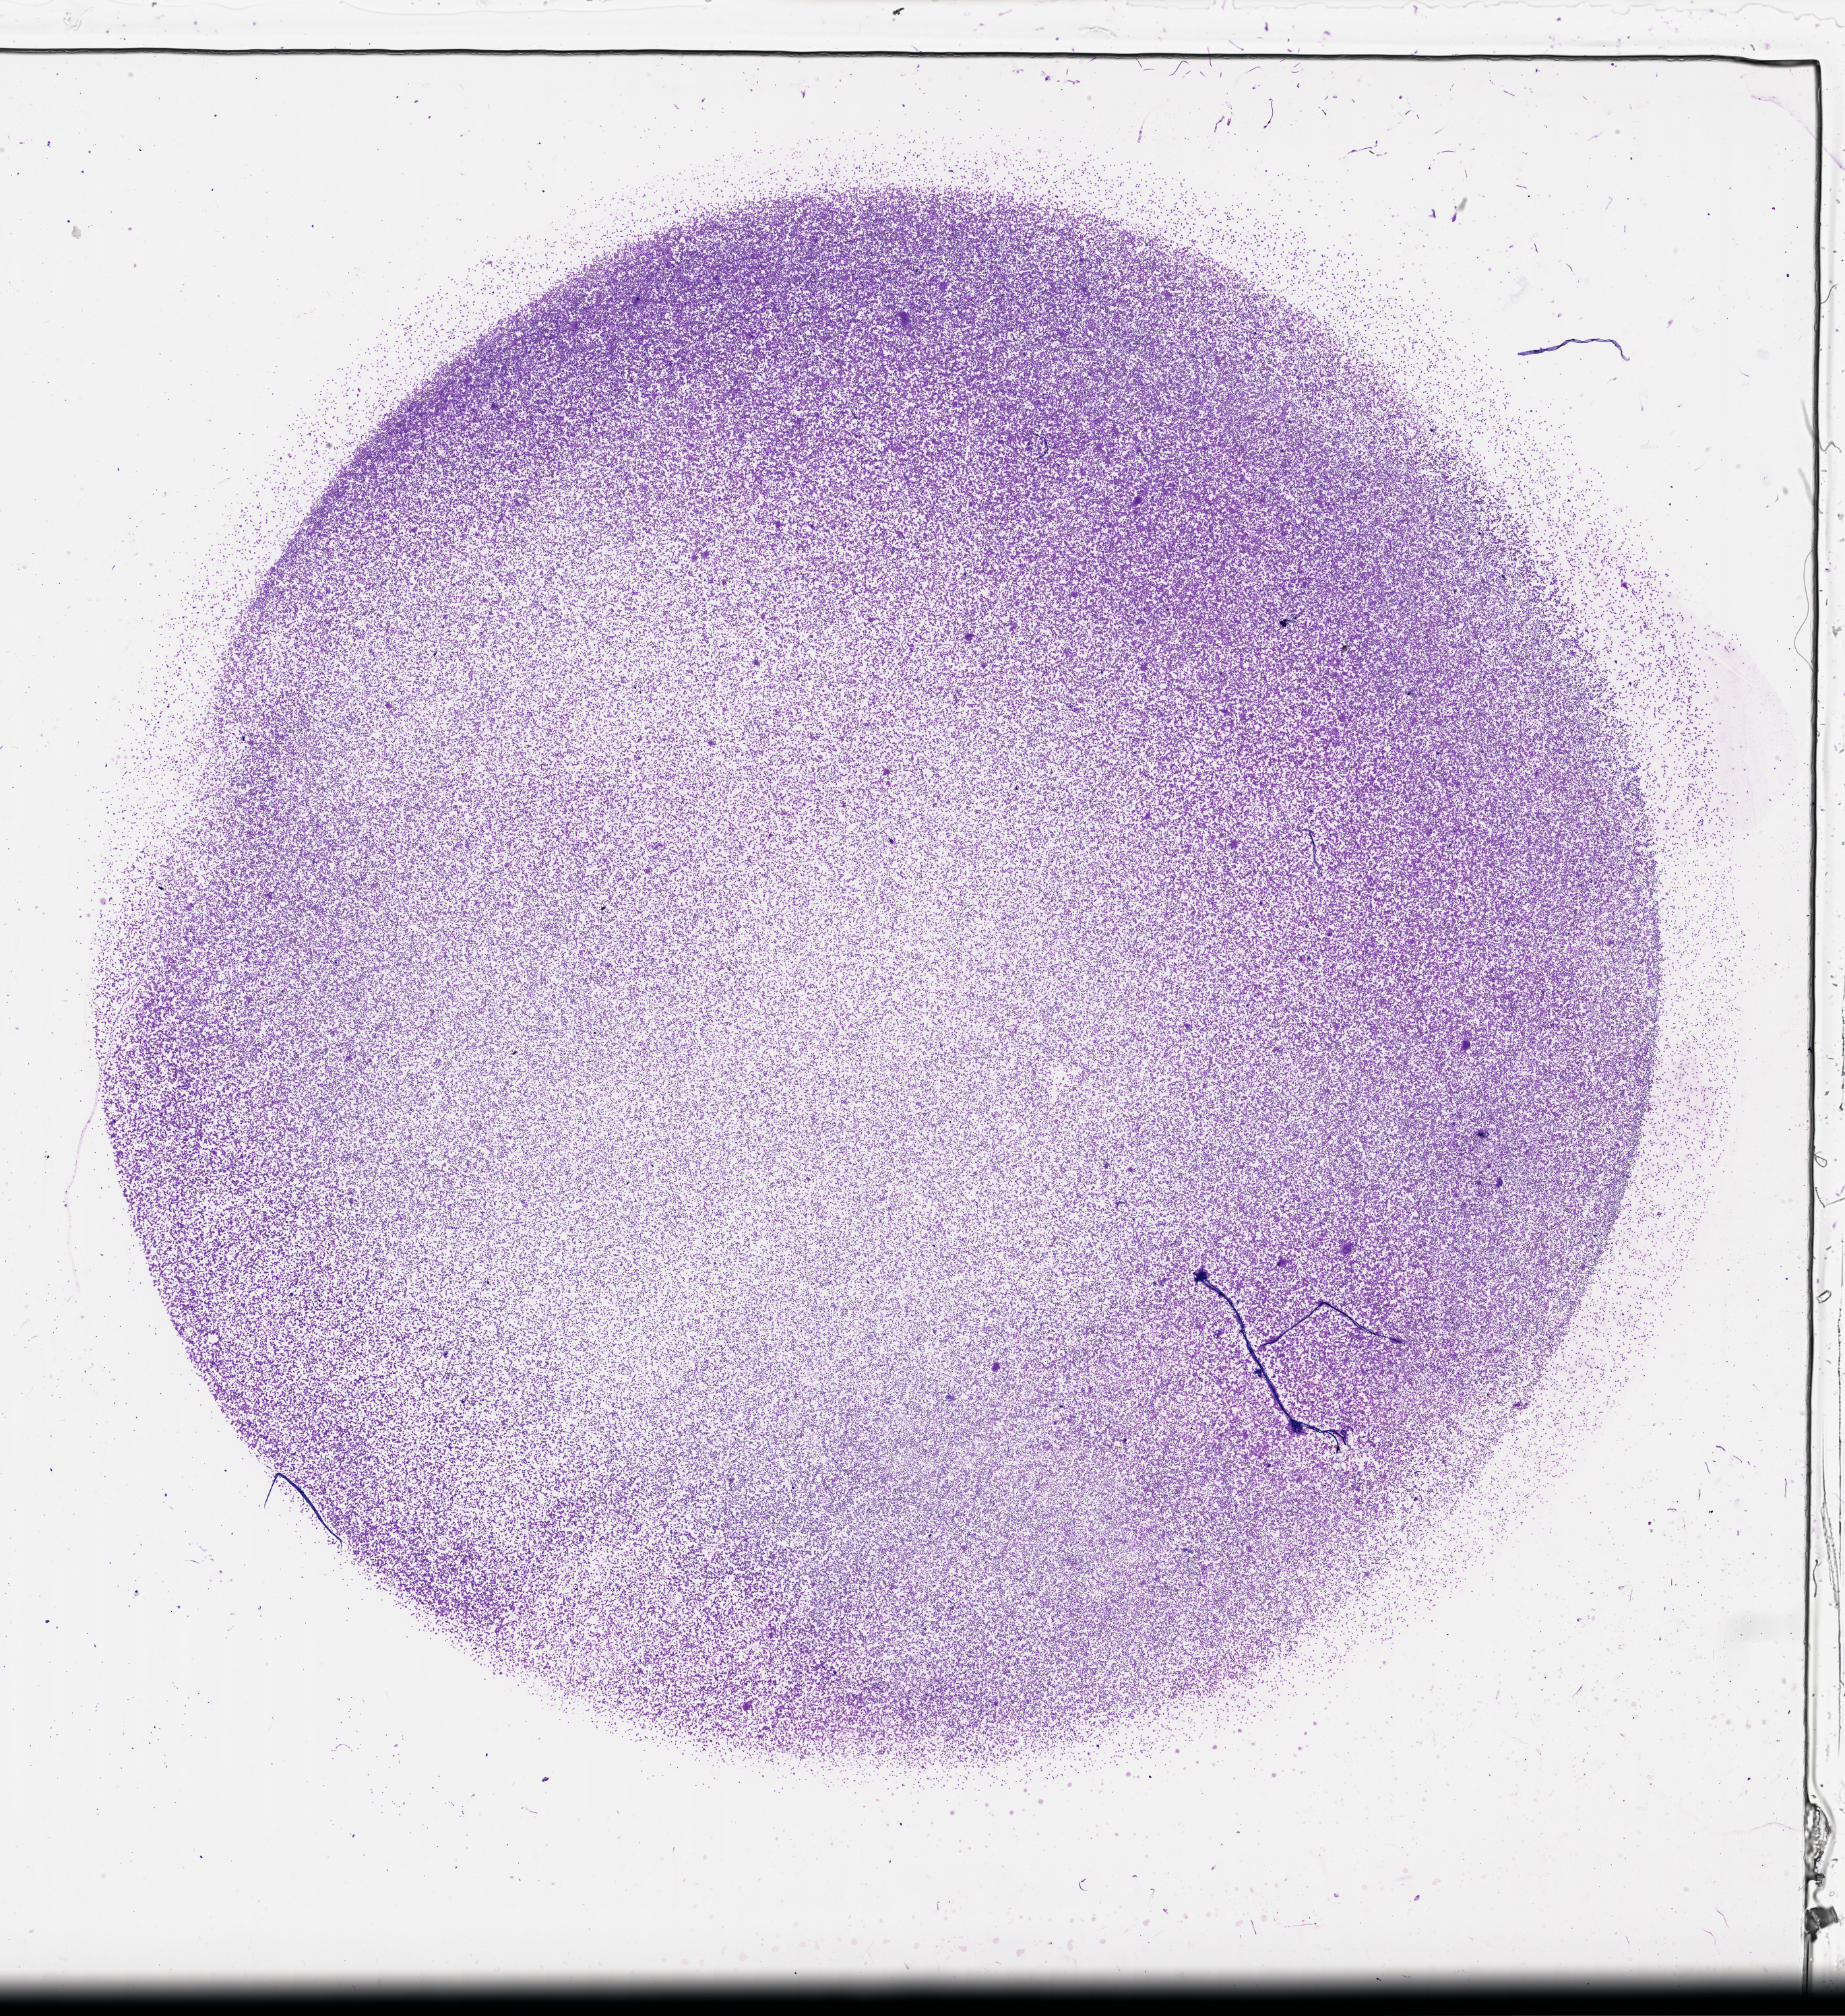
Digitized H&E tissue section (whole slide), a low-resolution overview of the entire scanned area, about 22.1 x 24.2 mm; bone marrow (leukaemic) sample. 79-year-old female patient. Blasts: 80%.
WHO classification: AML with maturation. Diagnosis: Acute Myeloid Leukemia. FAB classification: M2.